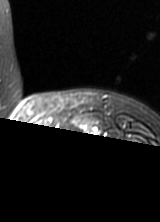
MRI of an extremity soft-tissue mass, one axial slice. Slice 58 of 69 in the series (ordered by position). T2-weighted fat-saturated. MR volume resampled by the dataset authors to the PET/CT grid (not the native acquisition matrix). 3.27 mm slice thickness. 160 × 222 image matrix, field of view 156 × 217 mm. Female patient. Case-level facts recorded for this patient, not image findings: histological type: pleomorphic leiomyosarcoma; grade: high; site of the primary tumour: left thigh.
Outlined on this slice (expert contour drawn on MRI and transferred to this co-registered scan by the dataset authors):
- gross tumour volume including surrounding oedema: bounding box [x1, y1, x2, y2] px = [36, 136, 51, 144]